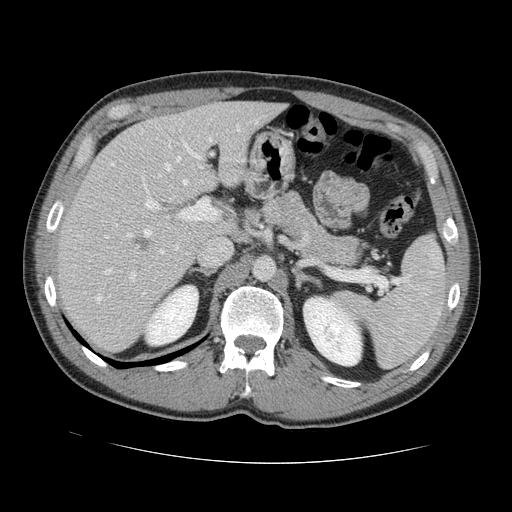
Contrast-enhanced abdominal CT, one axial slice; slice 85 of 131 in the series (ordered by position); 120 kVp; intravenous contrast given; soft-tissue window (W 400 / L 40 HU); 2.5 mm slice thickness; 512 × 512 image matrix, field of view 380 × 380 mm. Male patient, age 40 years. Case-level facts recorded for this patient, not image findings: diagnosis: colorectal cancer liver metastases, imaged before liver resection; multiple liver metastases: yes; largest metastasis: 2.9 cm; disease in both lobes: yes.
Annotated regions visible in this slice (manually delineated by an expert):
- hepatic veins: box from (x=96, y=156) to (x=188, y=301) px
- liver: (x=60, y=102)–(x=281, y=352)
- planned liver remnant (the part of the liver to remain after resection): (x=102, y=103)–(x=282, y=235)
- portal vein (with intrahepatic branches): (x=105, y=144)–(x=217, y=282)
- liver metastasis: (x=133, y=238)–(x=152, y=252)